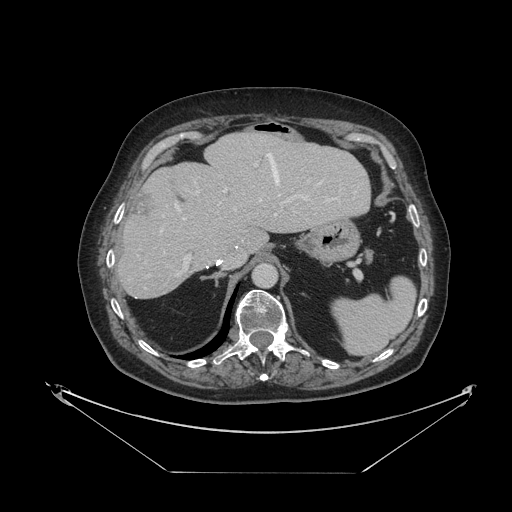
Contrast-enhanced abdominal CT, one axial slice; slice 74 of 121 in the series (ordered by position); reconstruction kernel STANDARD; 120 kVp; intravenous contrast given; soft-tissue window (W 400 / L 40 HU); 2.5 mm slice thickness; 512 × 512 image matrix. Male patient, age 68 years. From the clinical record (not read from this slice): diagnosis: colorectal cancer liver metastases, imaged before liver resection; multiple liver metastases: no; largest metastasis: 4 cm; chemotherapy before resection: yes.
Outlined on this slice (expert manual segmentation):
- hepatic veins: bounding box [x1, y1, x2, y2] px = [161, 153, 323, 233]
- liver: [119, 134, 370, 298]
- planned liver remnant (the part of the liver to remain after resection): [118, 134, 370, 298]
- portal vein (with intrahepatic branches): [174, 164, 308, 276]
- liver metastasis: [132, 191, 154, 219]